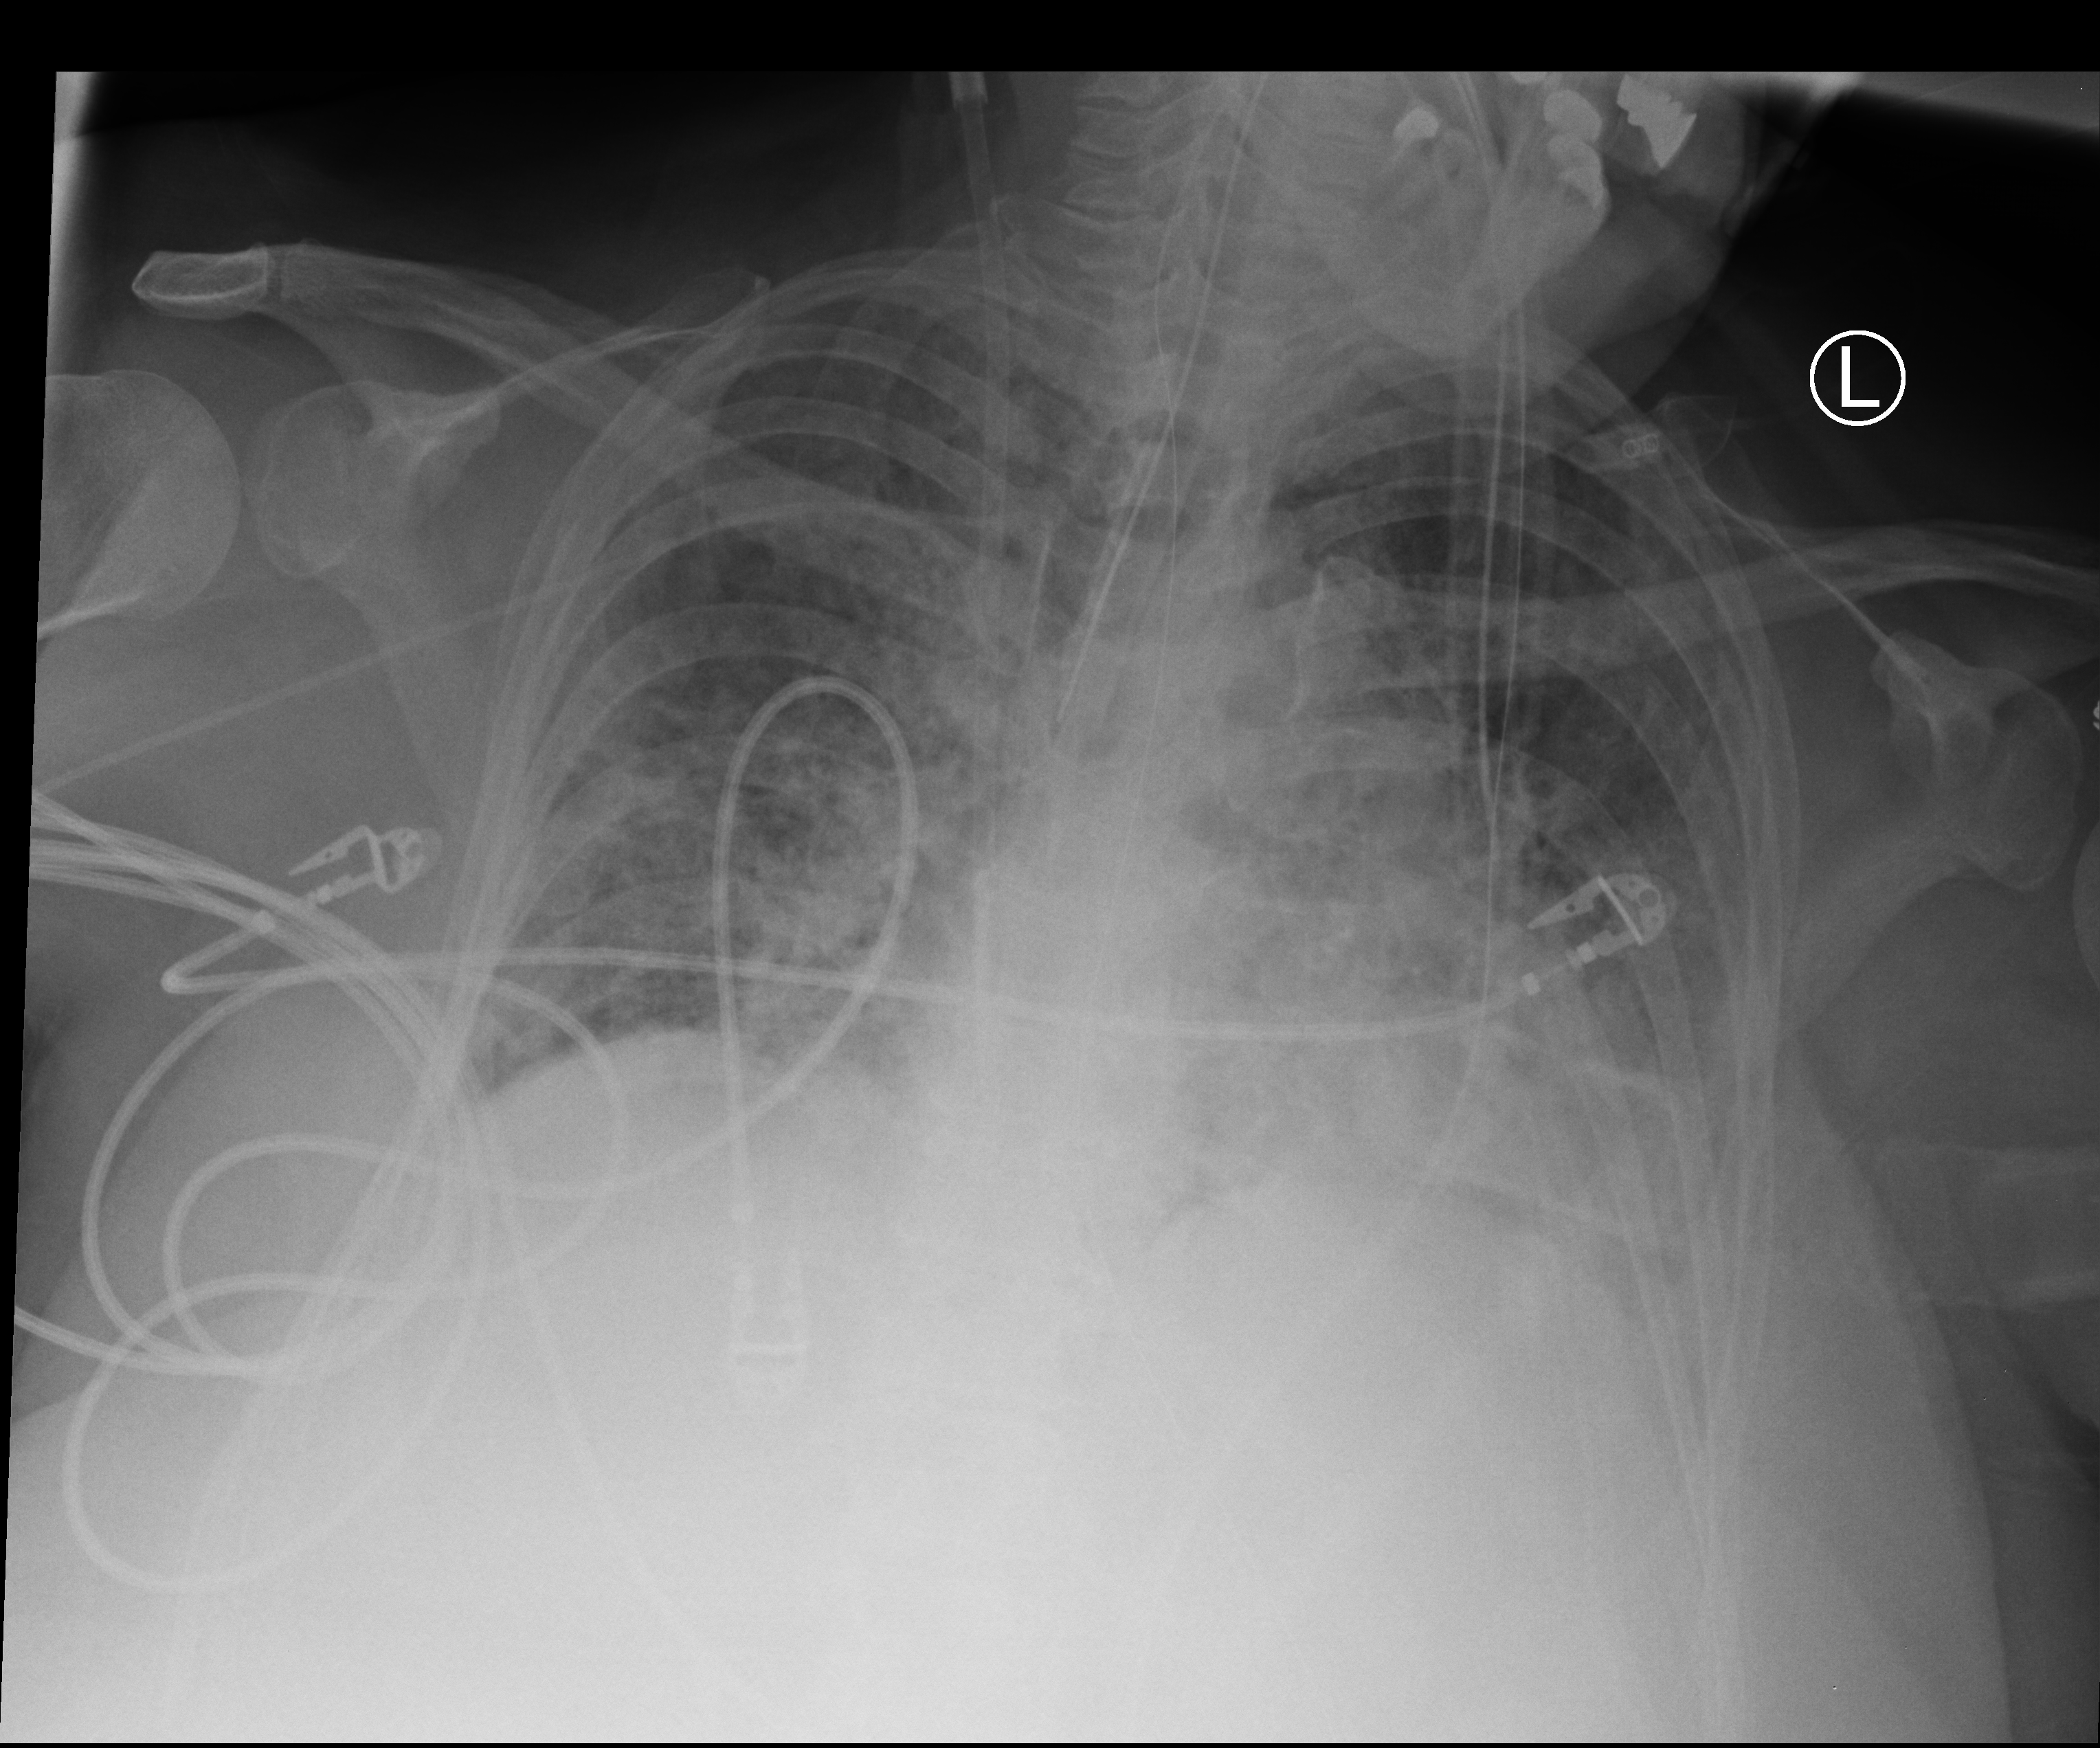
Chest X-ray (portable). Patient hospitalised with COVID-19; female, aged 60–74 years.
Hospital-stay facts (about this admission, not read from this image; timing relative to this image not recorded): admitted to intensive care during this hospital stay: yes; diabetes (admission record): no; mechanically ventilated during this hospital stay: yes.